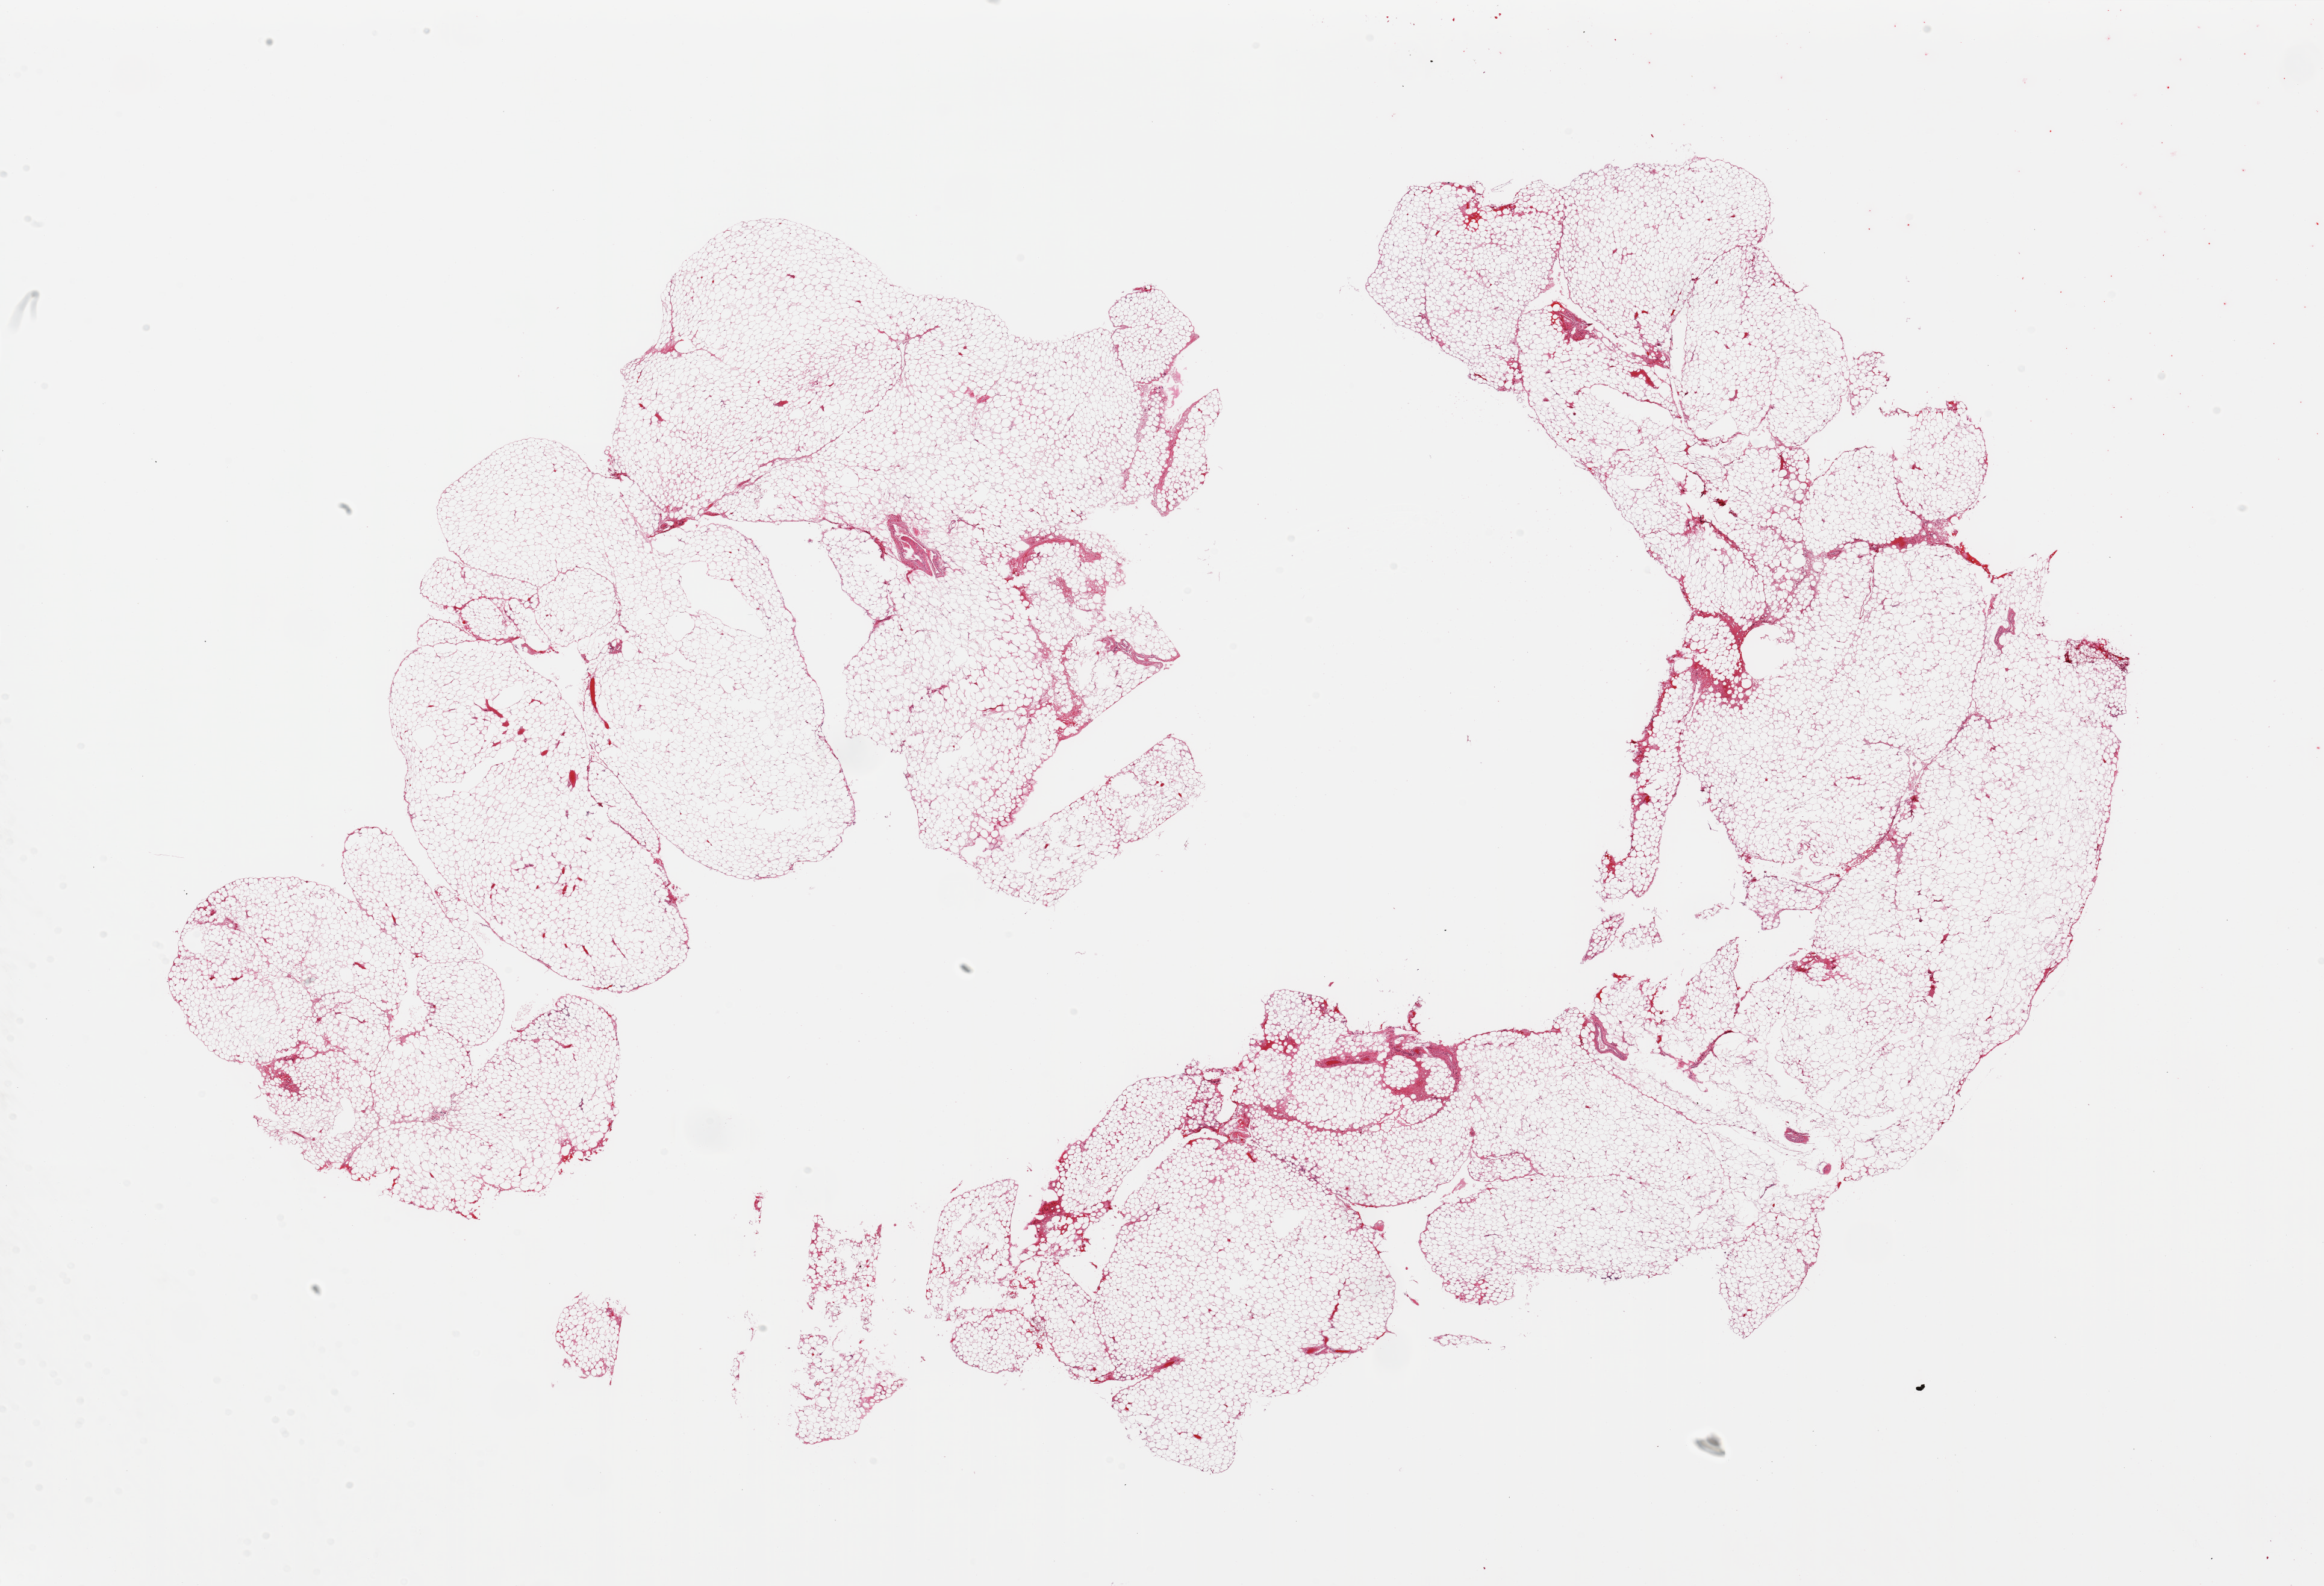
Haematoxylin and eosin whole-slide image, a low-resolution overview of the entire scanned area, about 30.5 x 20.8 mm (acquisition: 20x scan). PAXgene-fixed paraffin-embedded (PFPE) section. Target tissue: omentum. Tissue donor sample. Donor sex: male.
Pathologist's review note for this sample: 2 pieces, minimal fascia/vascular elements.